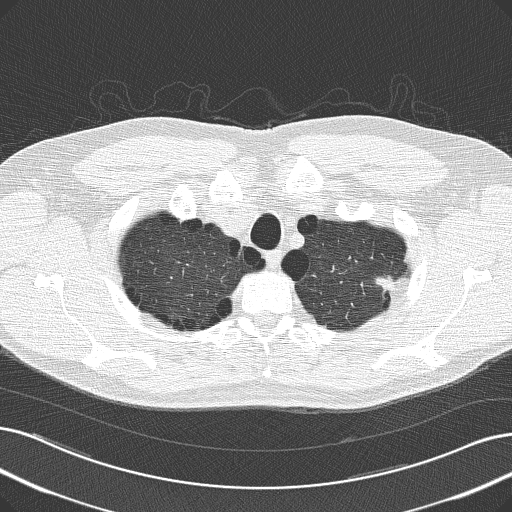
Axial slice from a low-dose chest CT screening exam, first (baseline) screen, lung window (W 1500 / L -600 HU), 2 mm slice thickness, 512 × 512 image matrix. Male participant, aged 62 years at enrolment. Current smoker at enrolment.
• Lesion marked by an expert reader, bounding box [x1, y1, x2, y2] px = [355, 256, 409, 309].
• The screening reader recorded 4 non-calcified nodules or masses ≥4 mm on this exam (left upper lobe, right upper lobe, right upper lobe, right middle lobe); which of them this box marks is not recorded.
• Official screen result: positive, change unspecified: nodule(s) >= 4 mm or enlarging nodule(s), mass(es), or other non-specific abnormalities suspicious for lung cancer.
• Lung cancer was diagnosed 383 days after this screen (after the second annual screen): adenocarcinoma, NOS, left upper lobe, well differentiated (G1), stage IB (AJCC 6th edition), 17 mm at pathology.